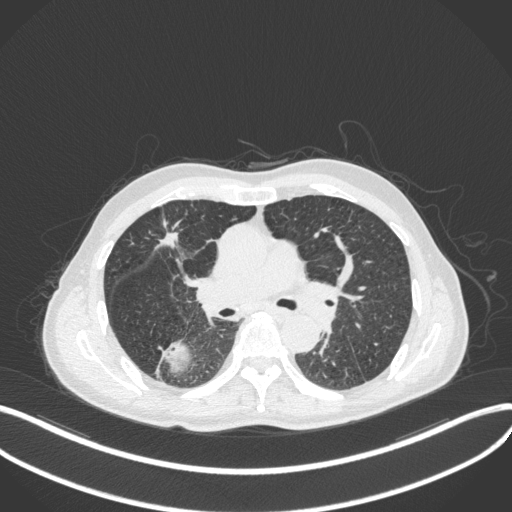
Chest CT, one axial slice. Slice 269 of 423 in the series (ordered by position). Reconstruction kernel B31f. 120 kVp. Lung window (W 1500 / L -600 HU). 1 mm slice thickness. 512 × 512 image matrix. Patient: male, 79 years. From the clinical record (not read from this slice): clinical TNM (as recorded): T3 N0 M0.
Annotated regions visible in this slice (bounding box drawn by a radiologist):
- lung tumour (recorded histology: adenocarcinoma): bounding box (x1, y1, x2, y2) in pixels: (155, 337, 194, 377)